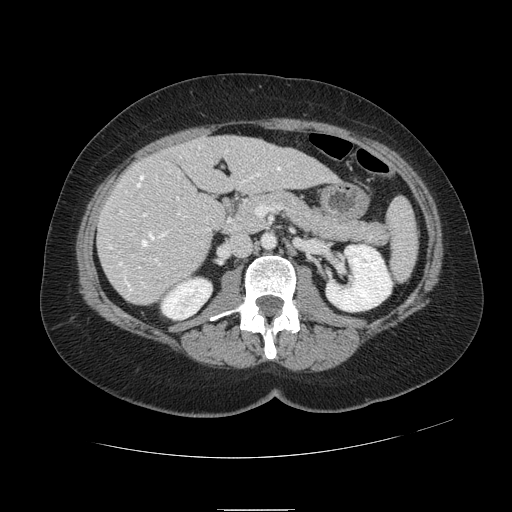
Contrast-enhanced abdominal CT, one axial slice. Slice 42 of 121 in the series (ordered by position). 120 kVp. Soft-tissue window (W 400 / L 40 HU). 512 × 512 image matrix, field of view 400 × 400 mm. Female patient, age 52 years. From the clinical record (not read from this slice): diagnosis: colorectal cancer liver metastases, imaged before liver resection; multiple liver metastases: yes; largest metastasis: 6.3 cm; chemotherapy before resection: yes.
Structures marked on this image (expert manual segmentation):
- hepatic veins: bounding box <109,151,280,286> (left, top, right, bottom; pixels)
- liver: <99,136,335,305>
- planned liver remnant (the part of the liver to remain after resection): <178,136,336,194>
- portal vein (with intrahepatic branches): <138,197,181,269>